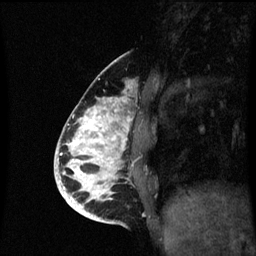
Breast MRI (dynamic contrast-enhanced), one sagittal slice. Position 25 of 60 along the scan axis. Dynamic contrast-enhanced series, image 2 of 3 at this slice position (ordered by acquisition). 1.5 T. TE 4.2 ms, TR 8.9 ms. 2 mm slice thickness. 256 × 256 image matrix, field of view 200 × 200 mm. Patient: female, 35 years. From the clinical record (not read from this slice): setting: breast cancer imaged before/during neoadjuvant chemotherapy; receptor status: HR-positive, HER2-negative.
Outlined on this slice (semi-automatically segmented with operator editing):
- analysis volume of interest (the breast-tissue region the enhancement analysis was run in; not a lesion): bounding box <66,98,135,215> (left, top, right, bottom; pixels)
- tumour enhancement mask (voxels above the 70 % enhancement threshold inside the analysis volume of interest): <66,98,131,215>